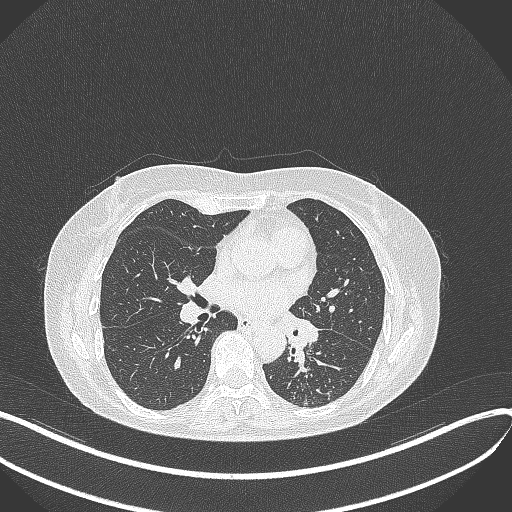
Chest CT, one axial slice; position 210 of 429 along the scan axis; reconstruction kernel B70f; 100 kVp; lung window (W 1500 / L -600 HU); 1 mm slice thickness; 512 × 512 image matrix, field of view 400 × 400 mm. Patient: female, 63 years. From the clinical record (not read from this slice): clinical TNM (as recorded): T1b N0 M0; histopathological grade: G2-3.
Outlined on this slice (rectangle marked by the reading radiologist):
- lung tumour (recorded histology: adenocarcinoma): bounding box <282,311,321,352> (left, top, right, bottom; pixels)